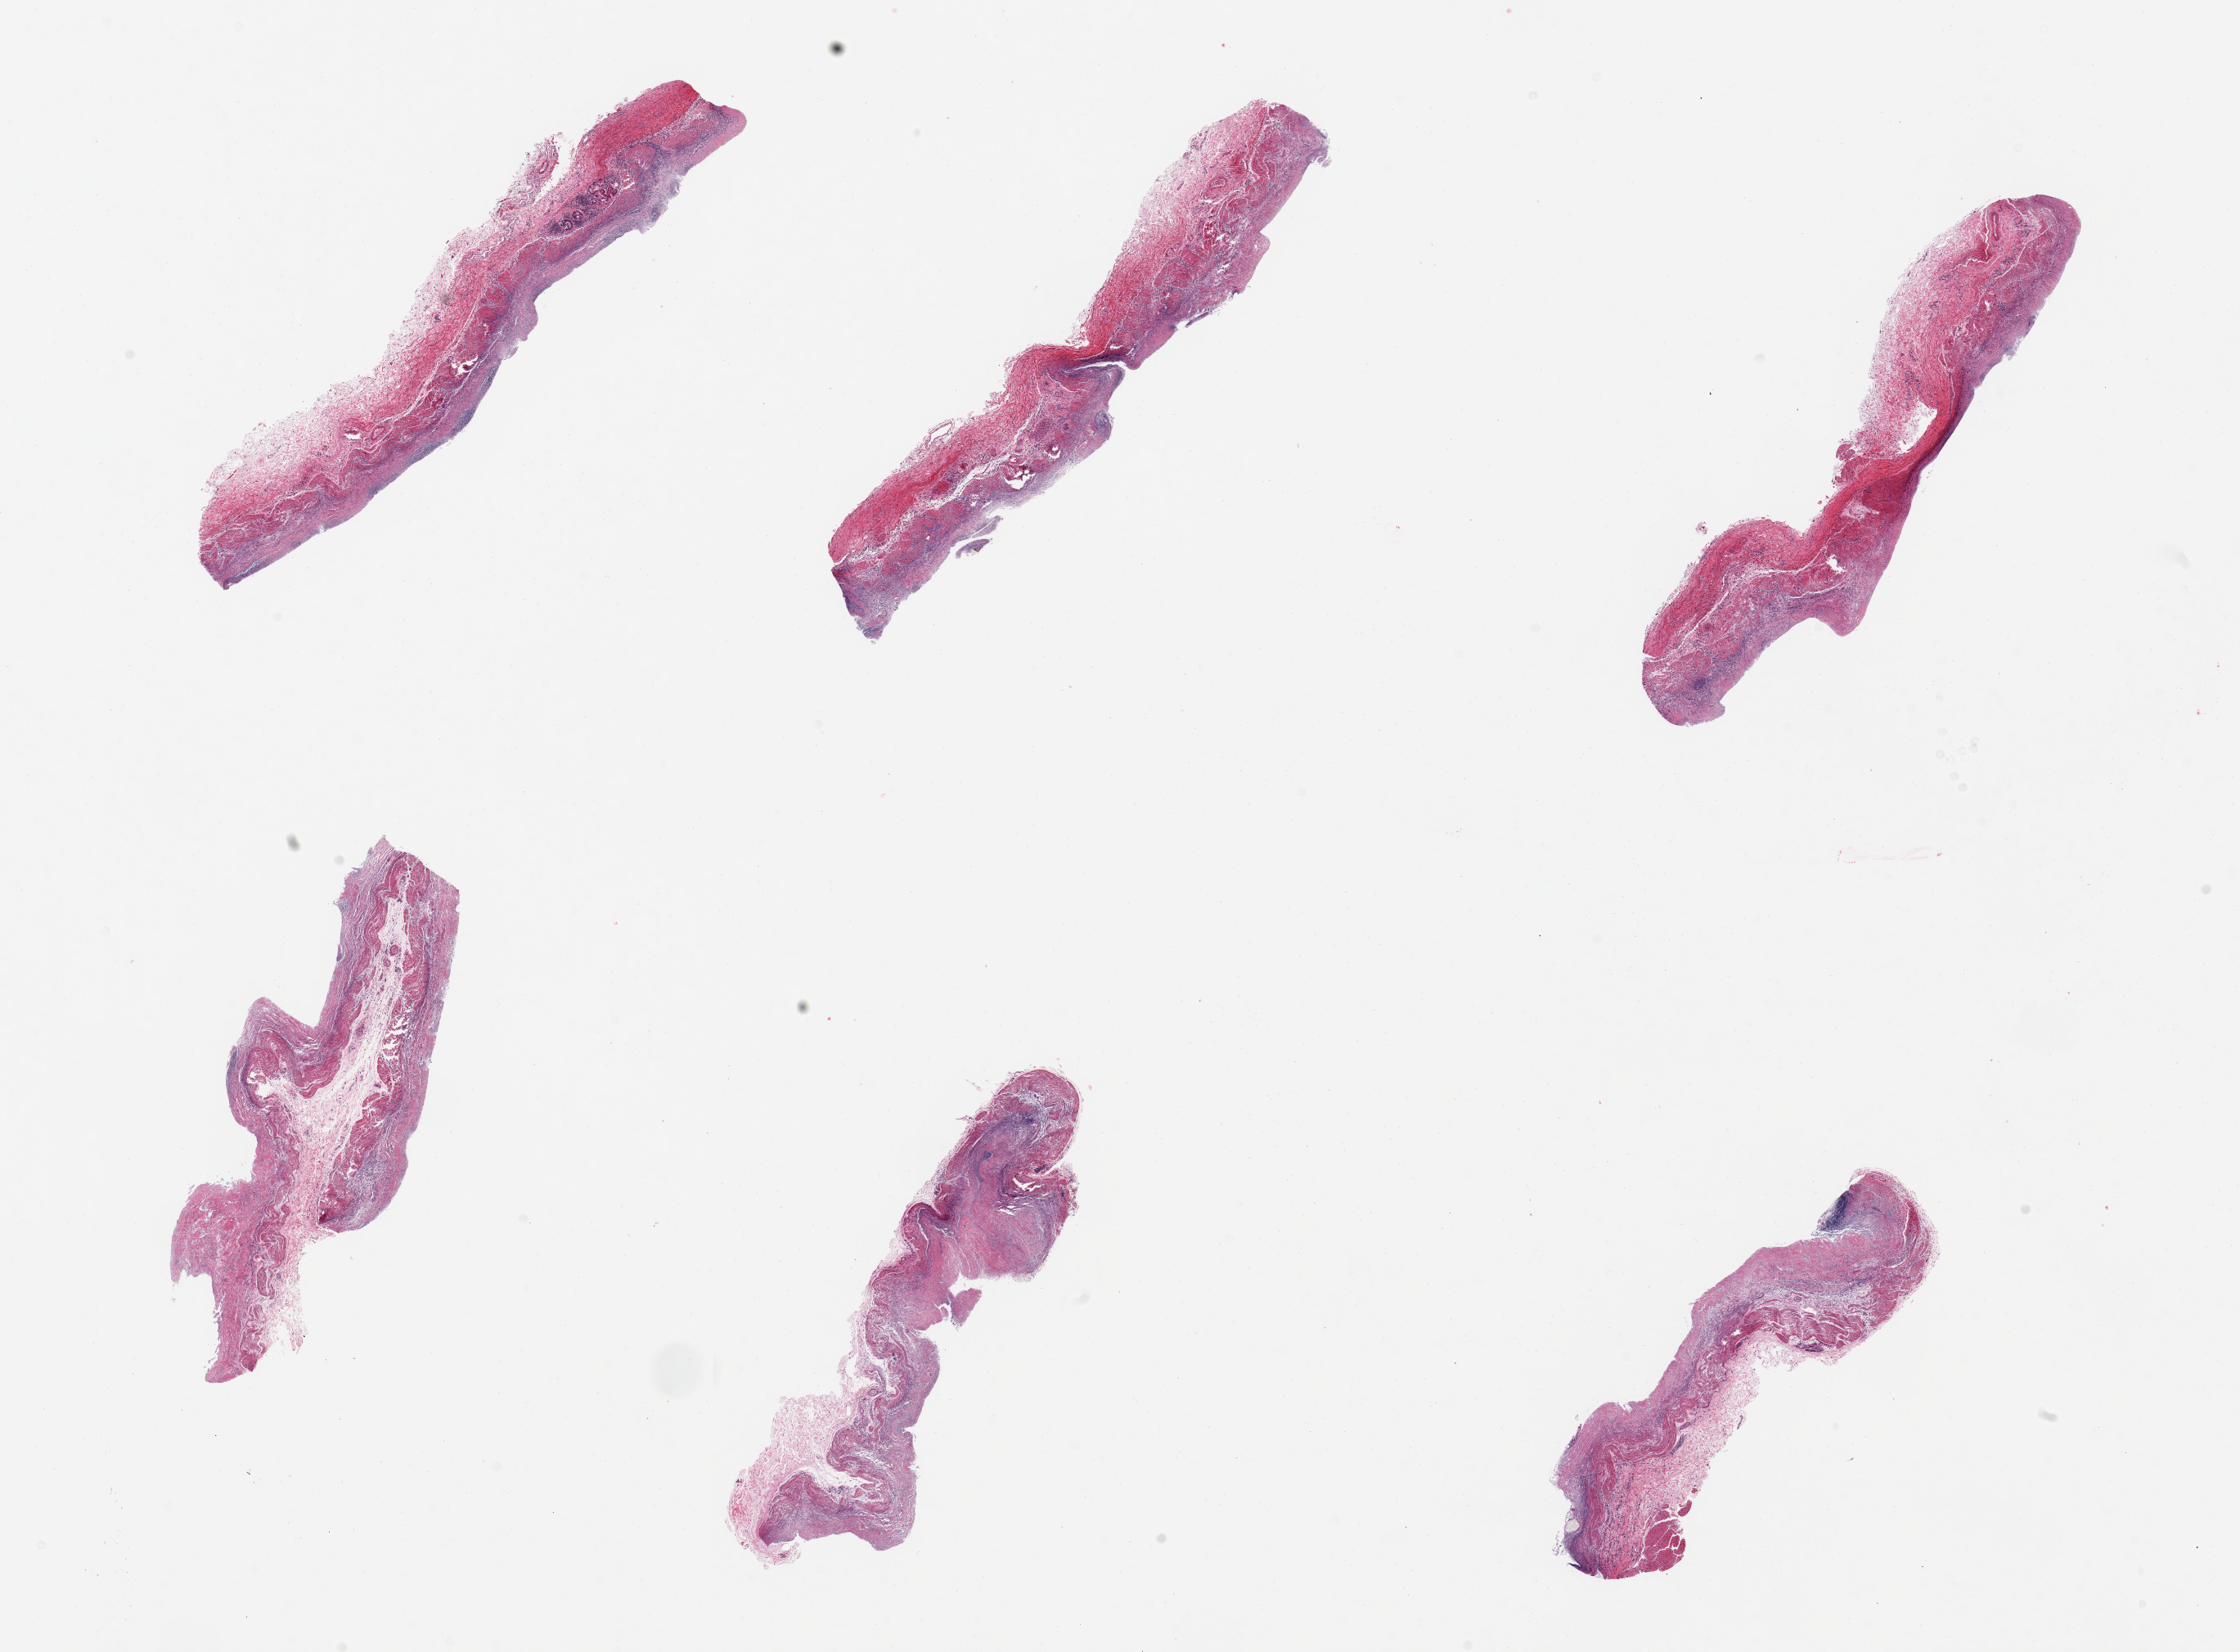
Digitized hematoxylin and eosin (H&E)-stained section — low-resolution overview of the scanned area, about 21.7 x 16.0 mm (acquisition: 20x scan); PAXgene-fixed, paraffin-embedded tissue; target tissue: esophageal mucous membrane; donor tissue sample. Donor sex: female.
Pathologist's review note for this sample: 6 pieces, sqaumous mucosa markedly and unusually autolyzed/sloughed.